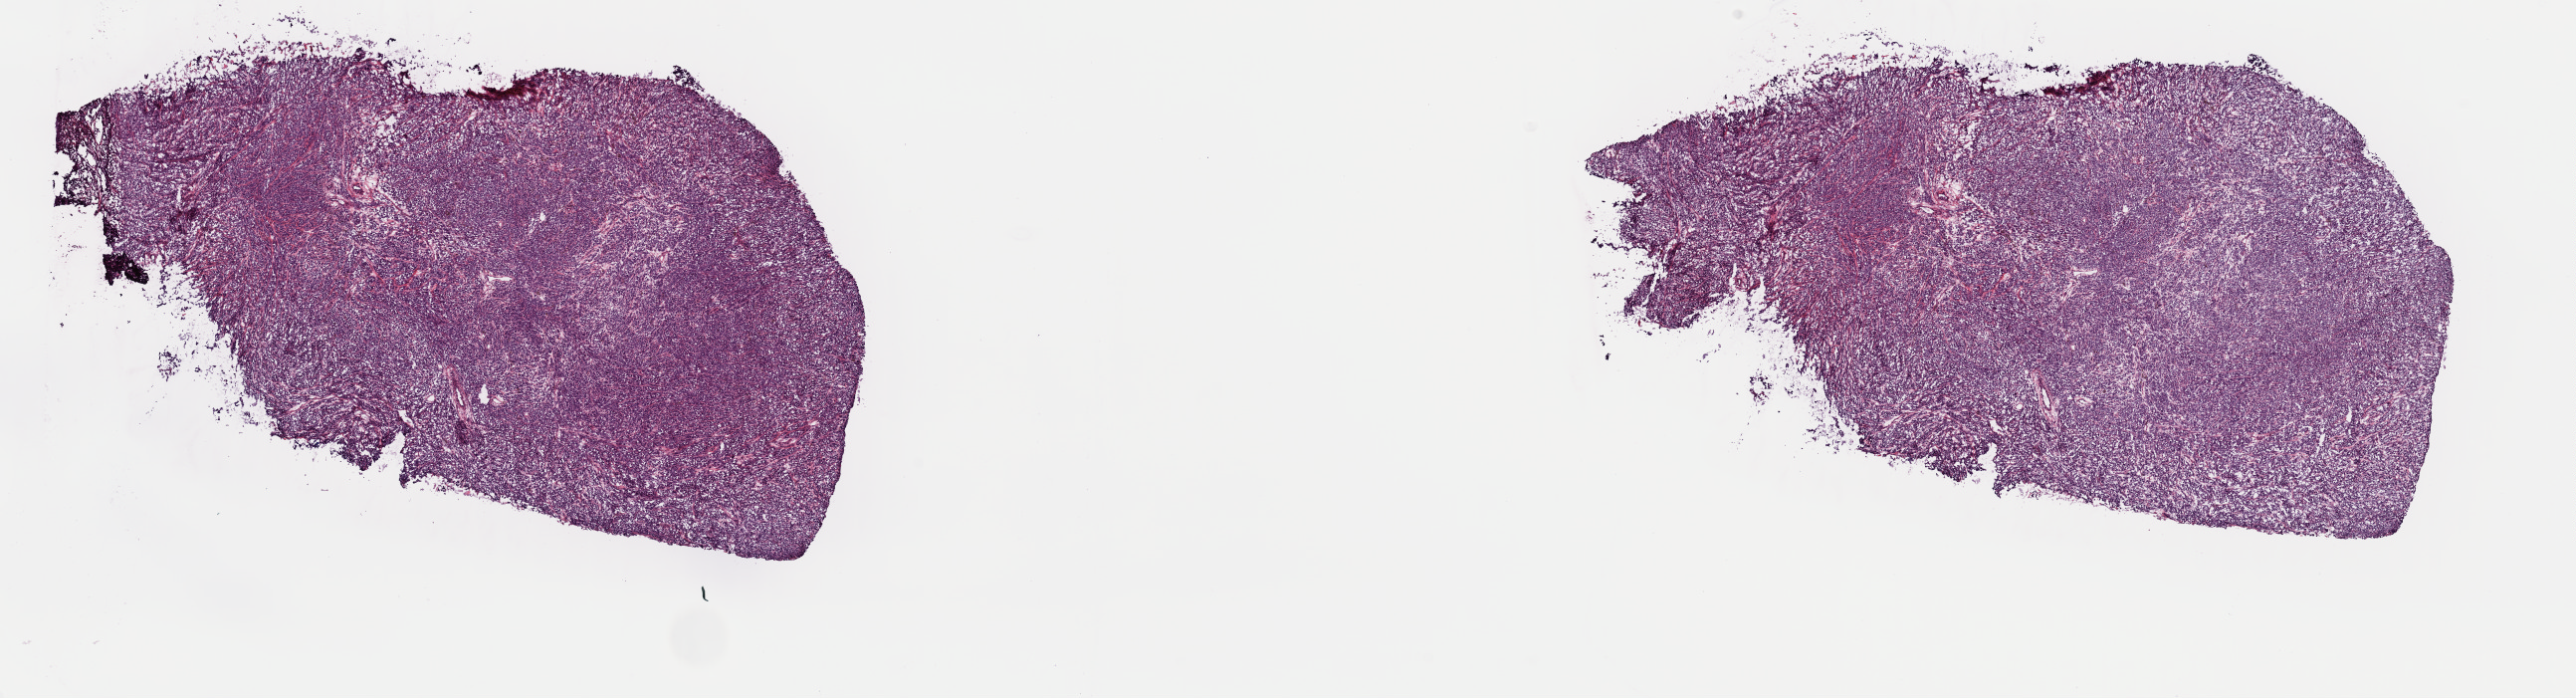
H&E-stained whole-slide image, whole scanned area (about 20.4 x 5.5 mm, from a 40x scan) shown as a low-resolution overview, frozen section from the top of the tissue portion, sample: primary tumour, skin. Patient: female, age at initial diagnosis 73 years. Composition of this section per pathologist review: tumour cells 100%, tumour nuclei 97%, normal cells 0%, stromal cells 0%, necrosis 0%. Inflammatory infiltration, as recorded: lymphocyte infiltration 0%, monocyte infiltration 0%, neutrophil infiltration 0%.
• AJCC pathologic stage: IIIC (7th edition)
• diagnosis: Nodular melanoma